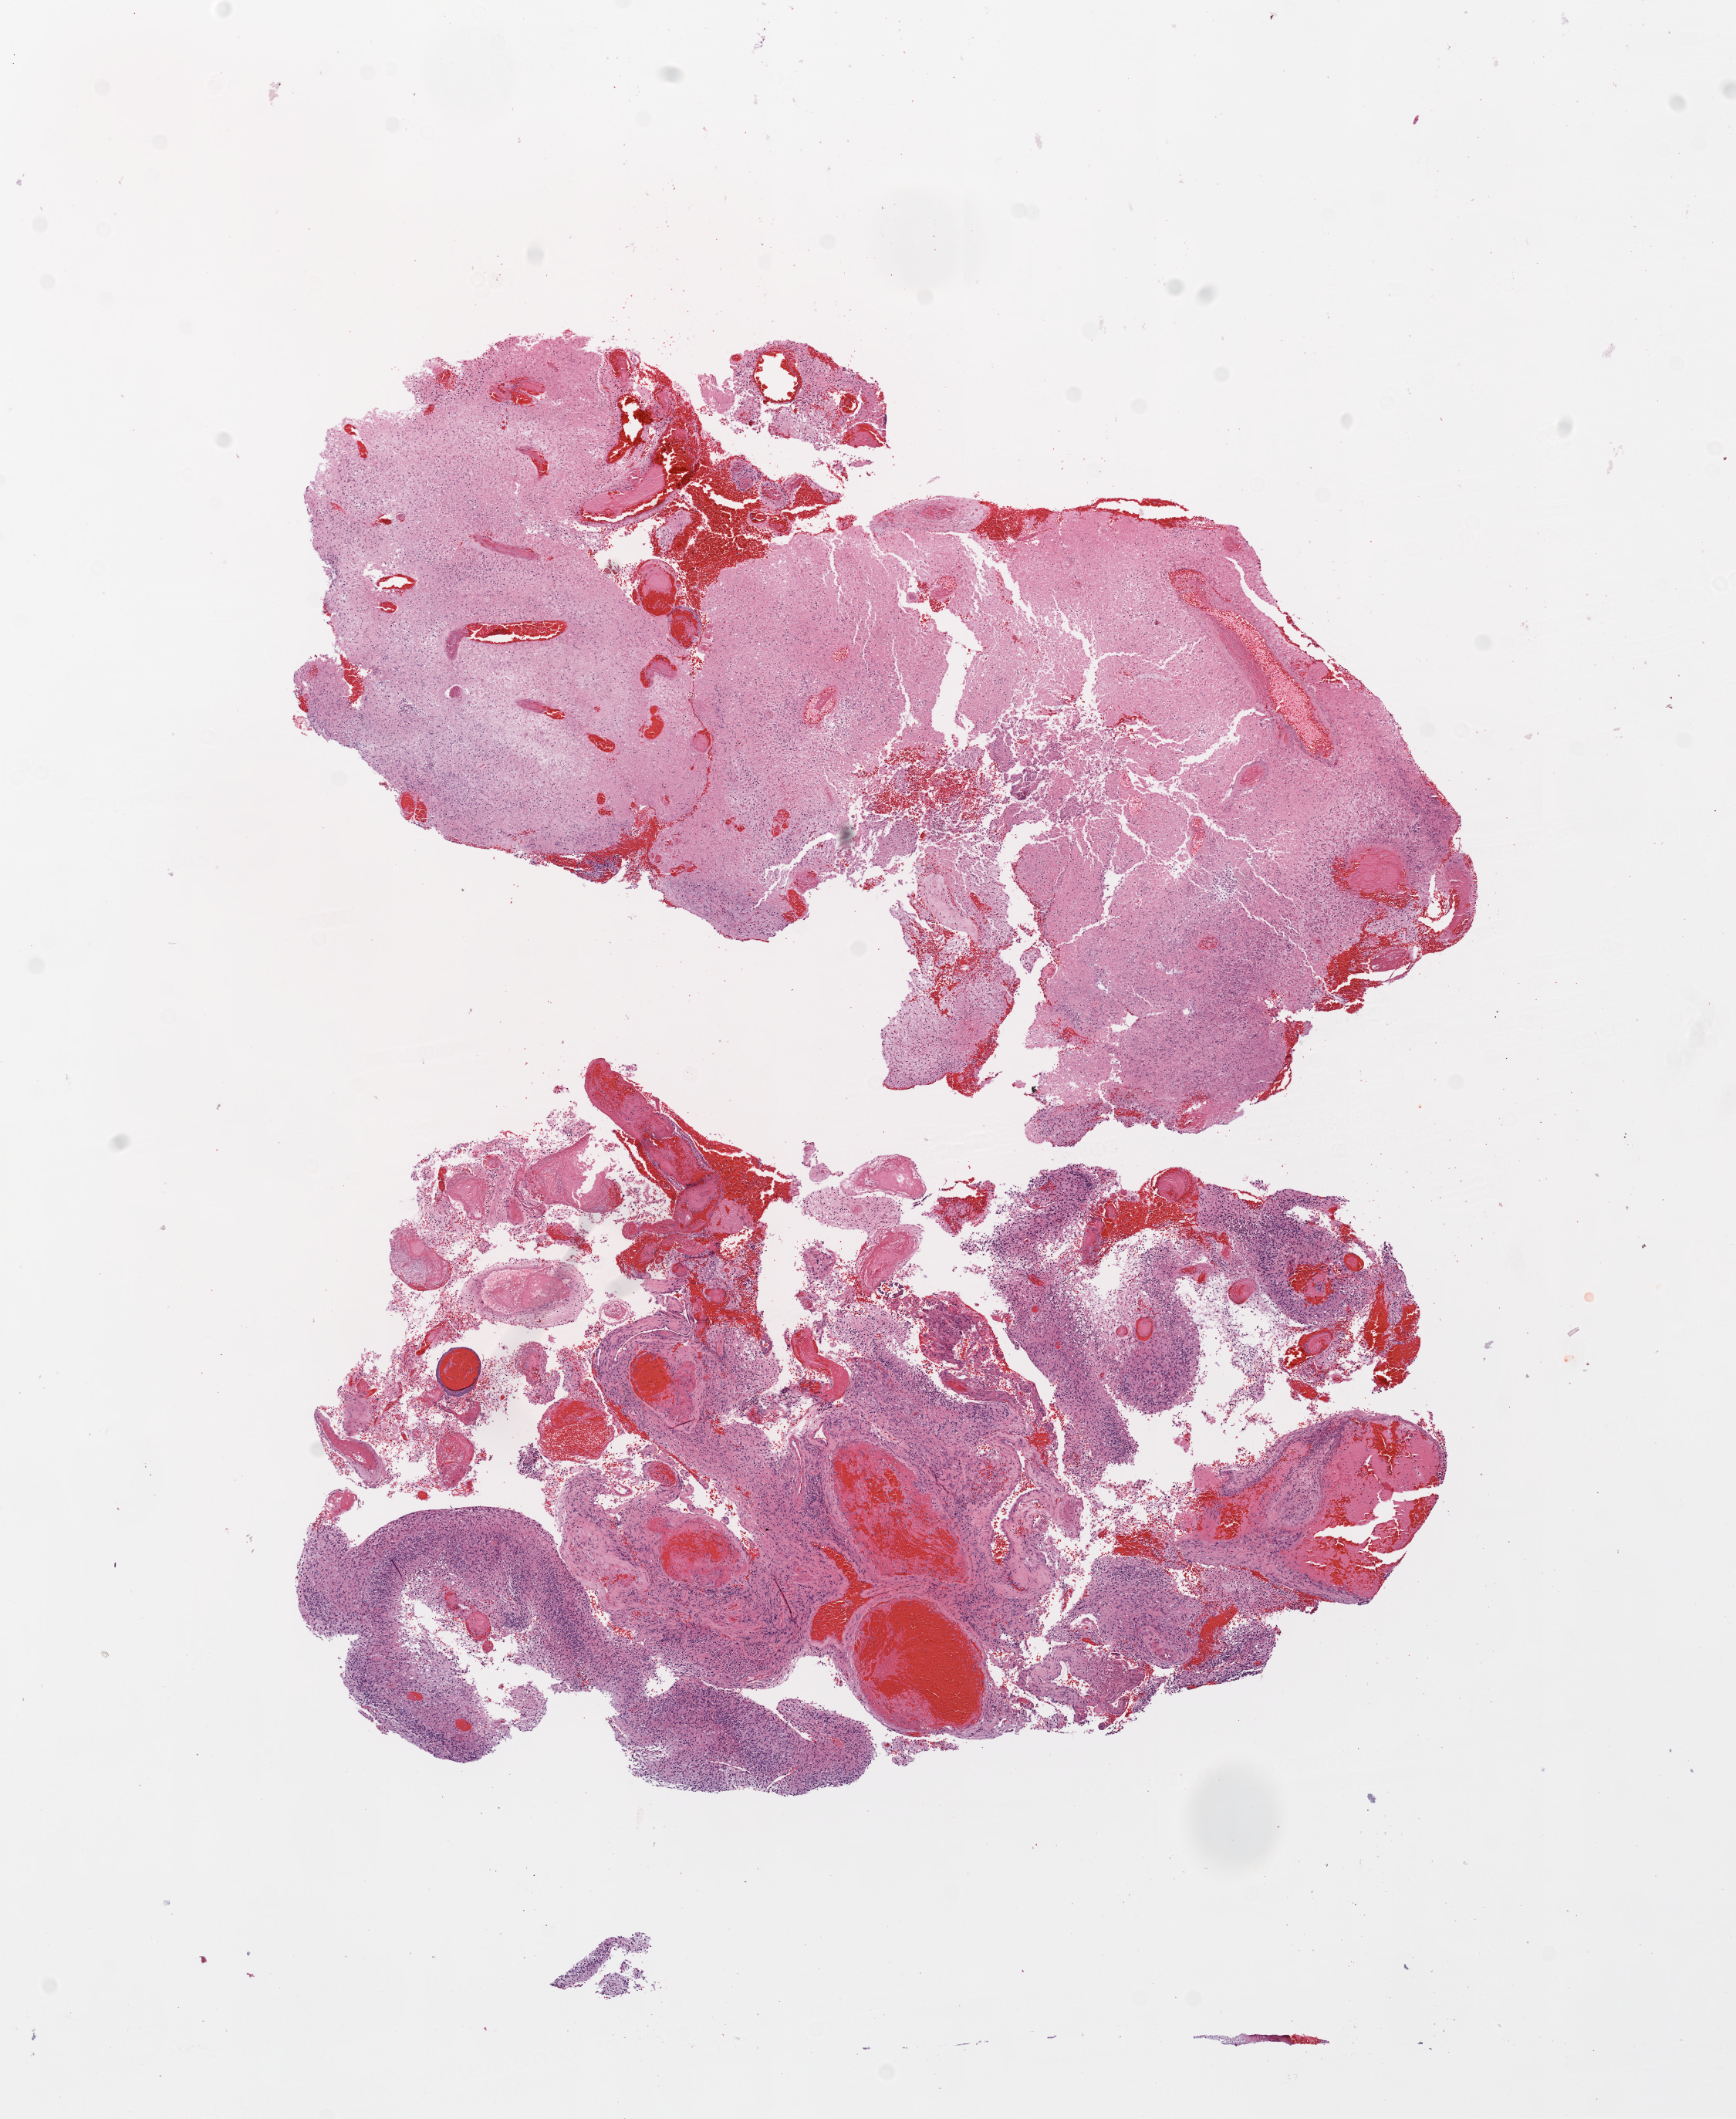
Digitized H&E-stained tissue section (whole slide), shown as a low-resolution overview of the whole scanned area (about 9.0 x 11.0 mm); formalin-fixed paraffin-embedded (FFPE) diagnostic section; brain, primary tumour sample. Male patient; age at initial diagnosis 58 years.
Pathologic diagnosis: Glioblastoma.